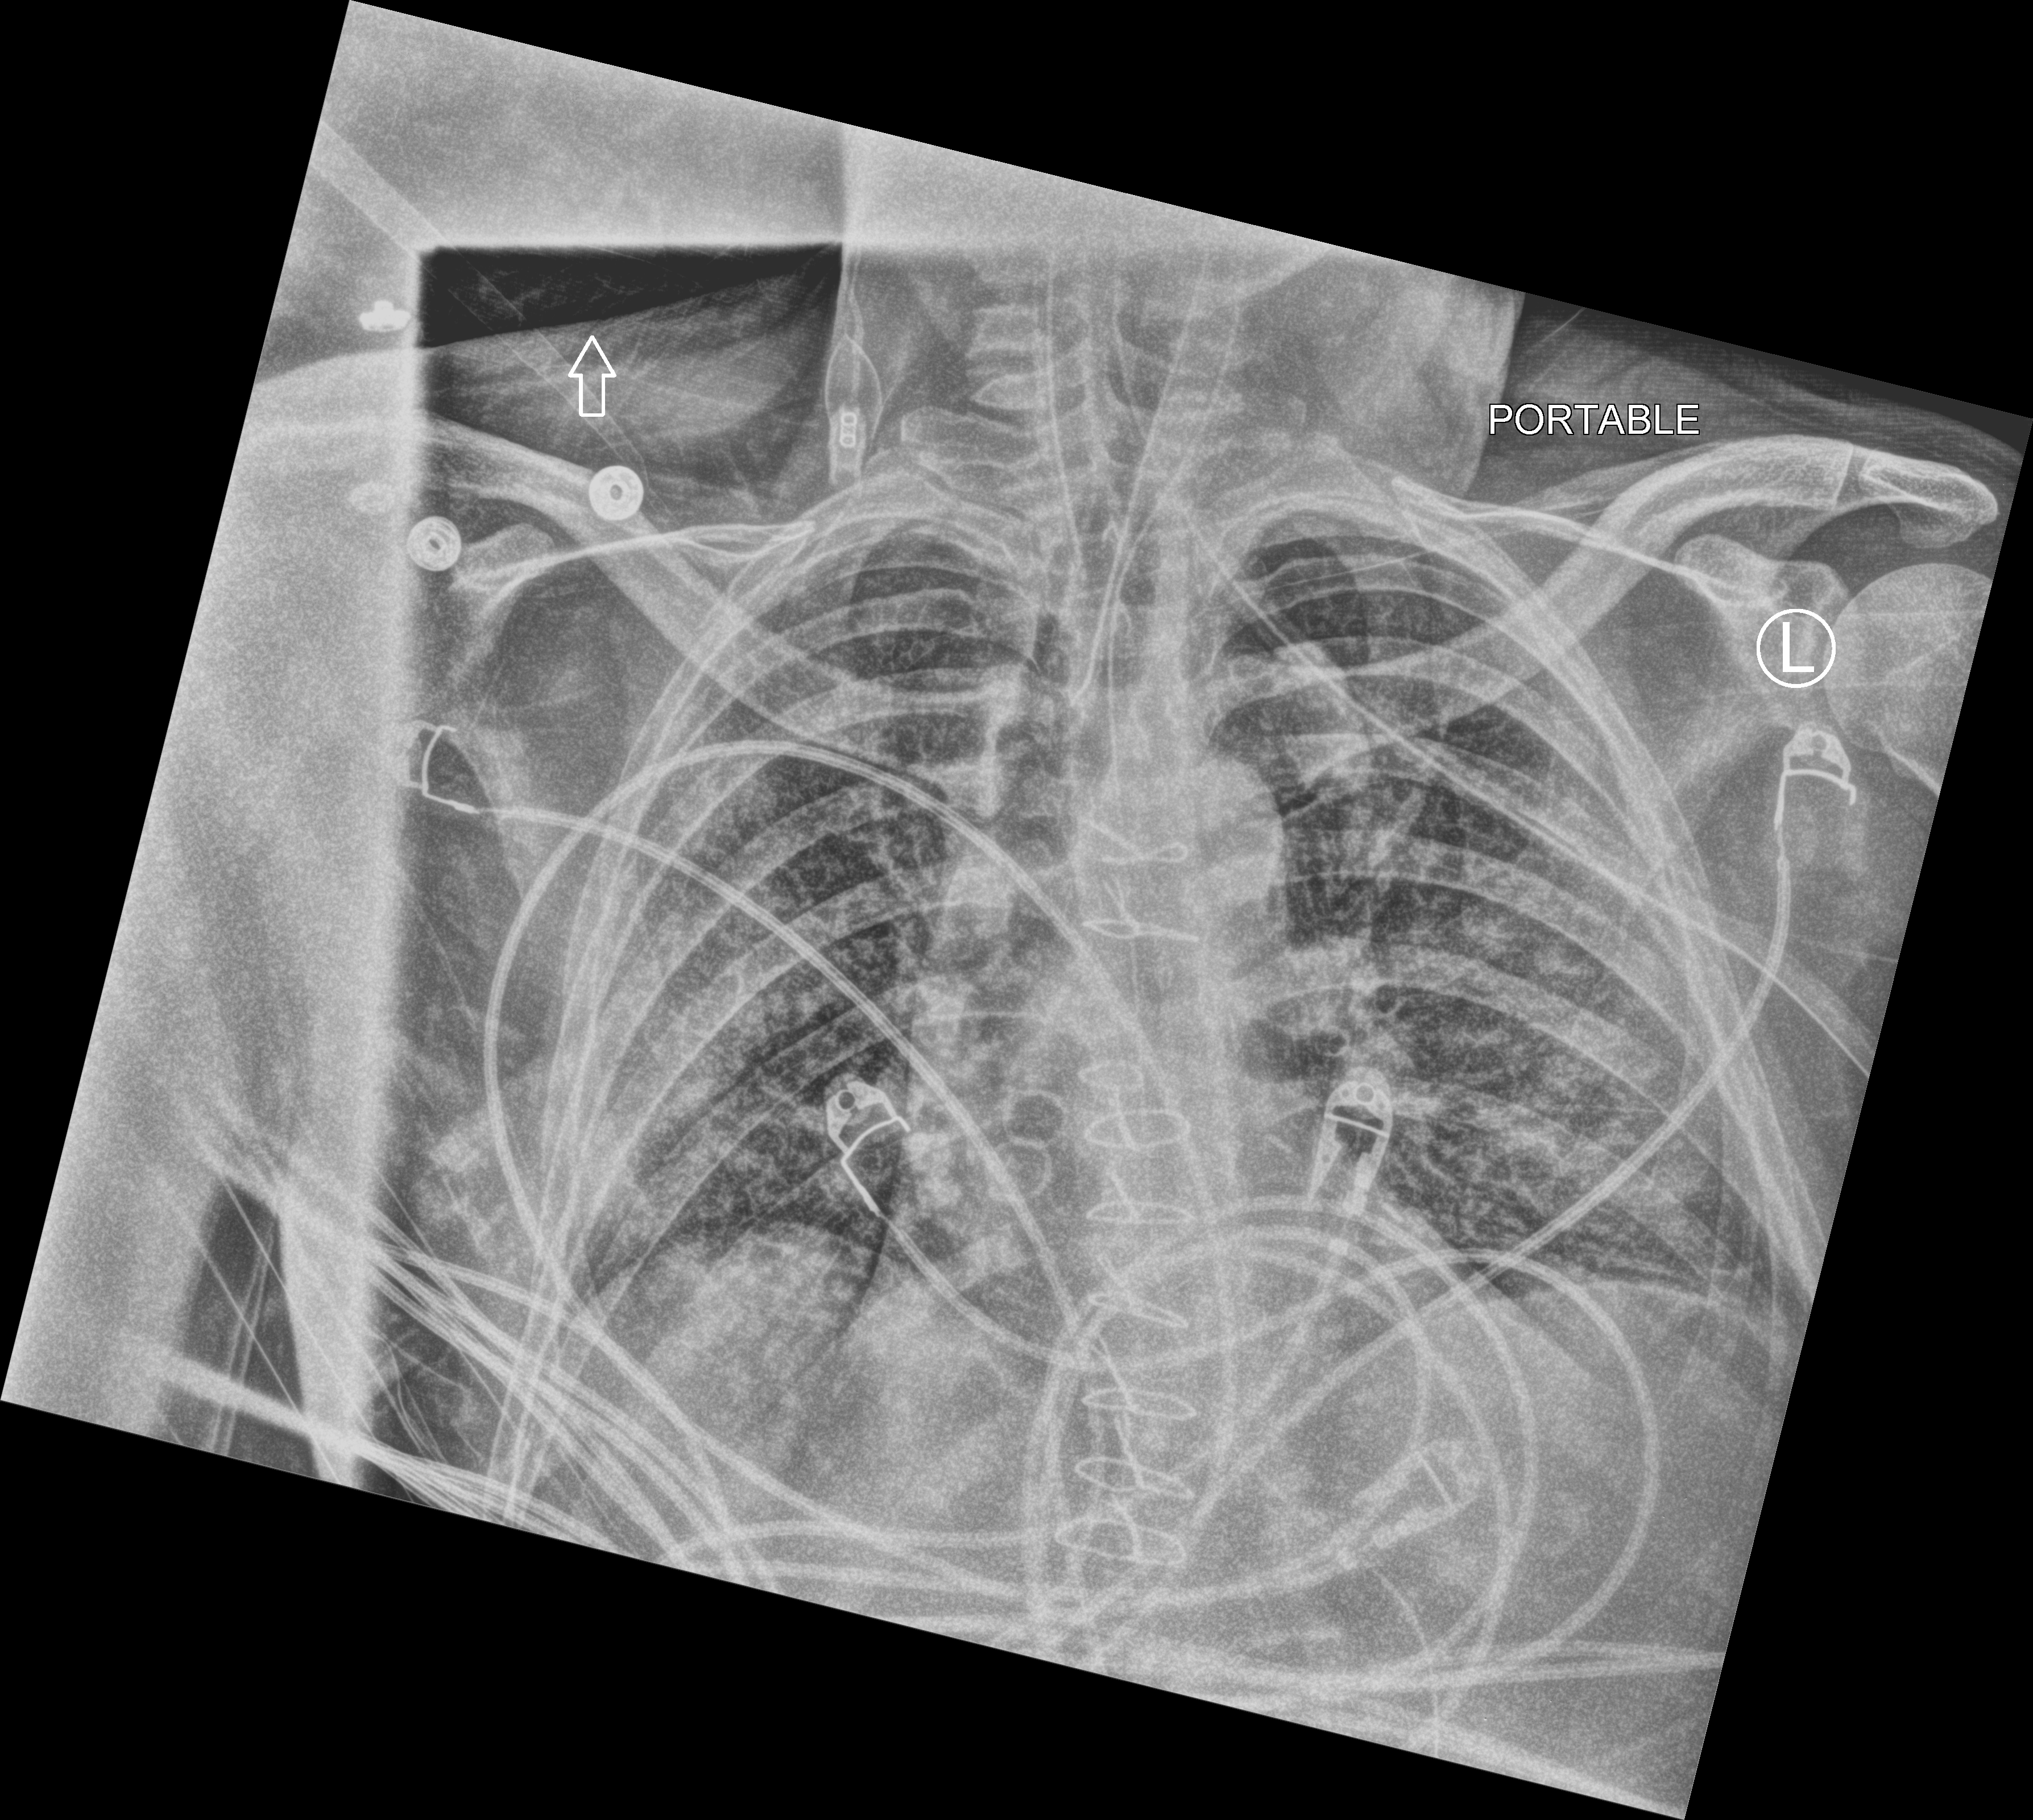
Bedside chest radiograph (computed radiography), anteroposterior (AP) projection. Male patient hospitalised with COVID-19, age 18–59 years.
From the hospital-stay record, not from the radiograph (when in the stay this image was taken is not recorded): mechanically ventilated during this hospital stay: yes; admitted to intensive care during this hospital stay: yes.